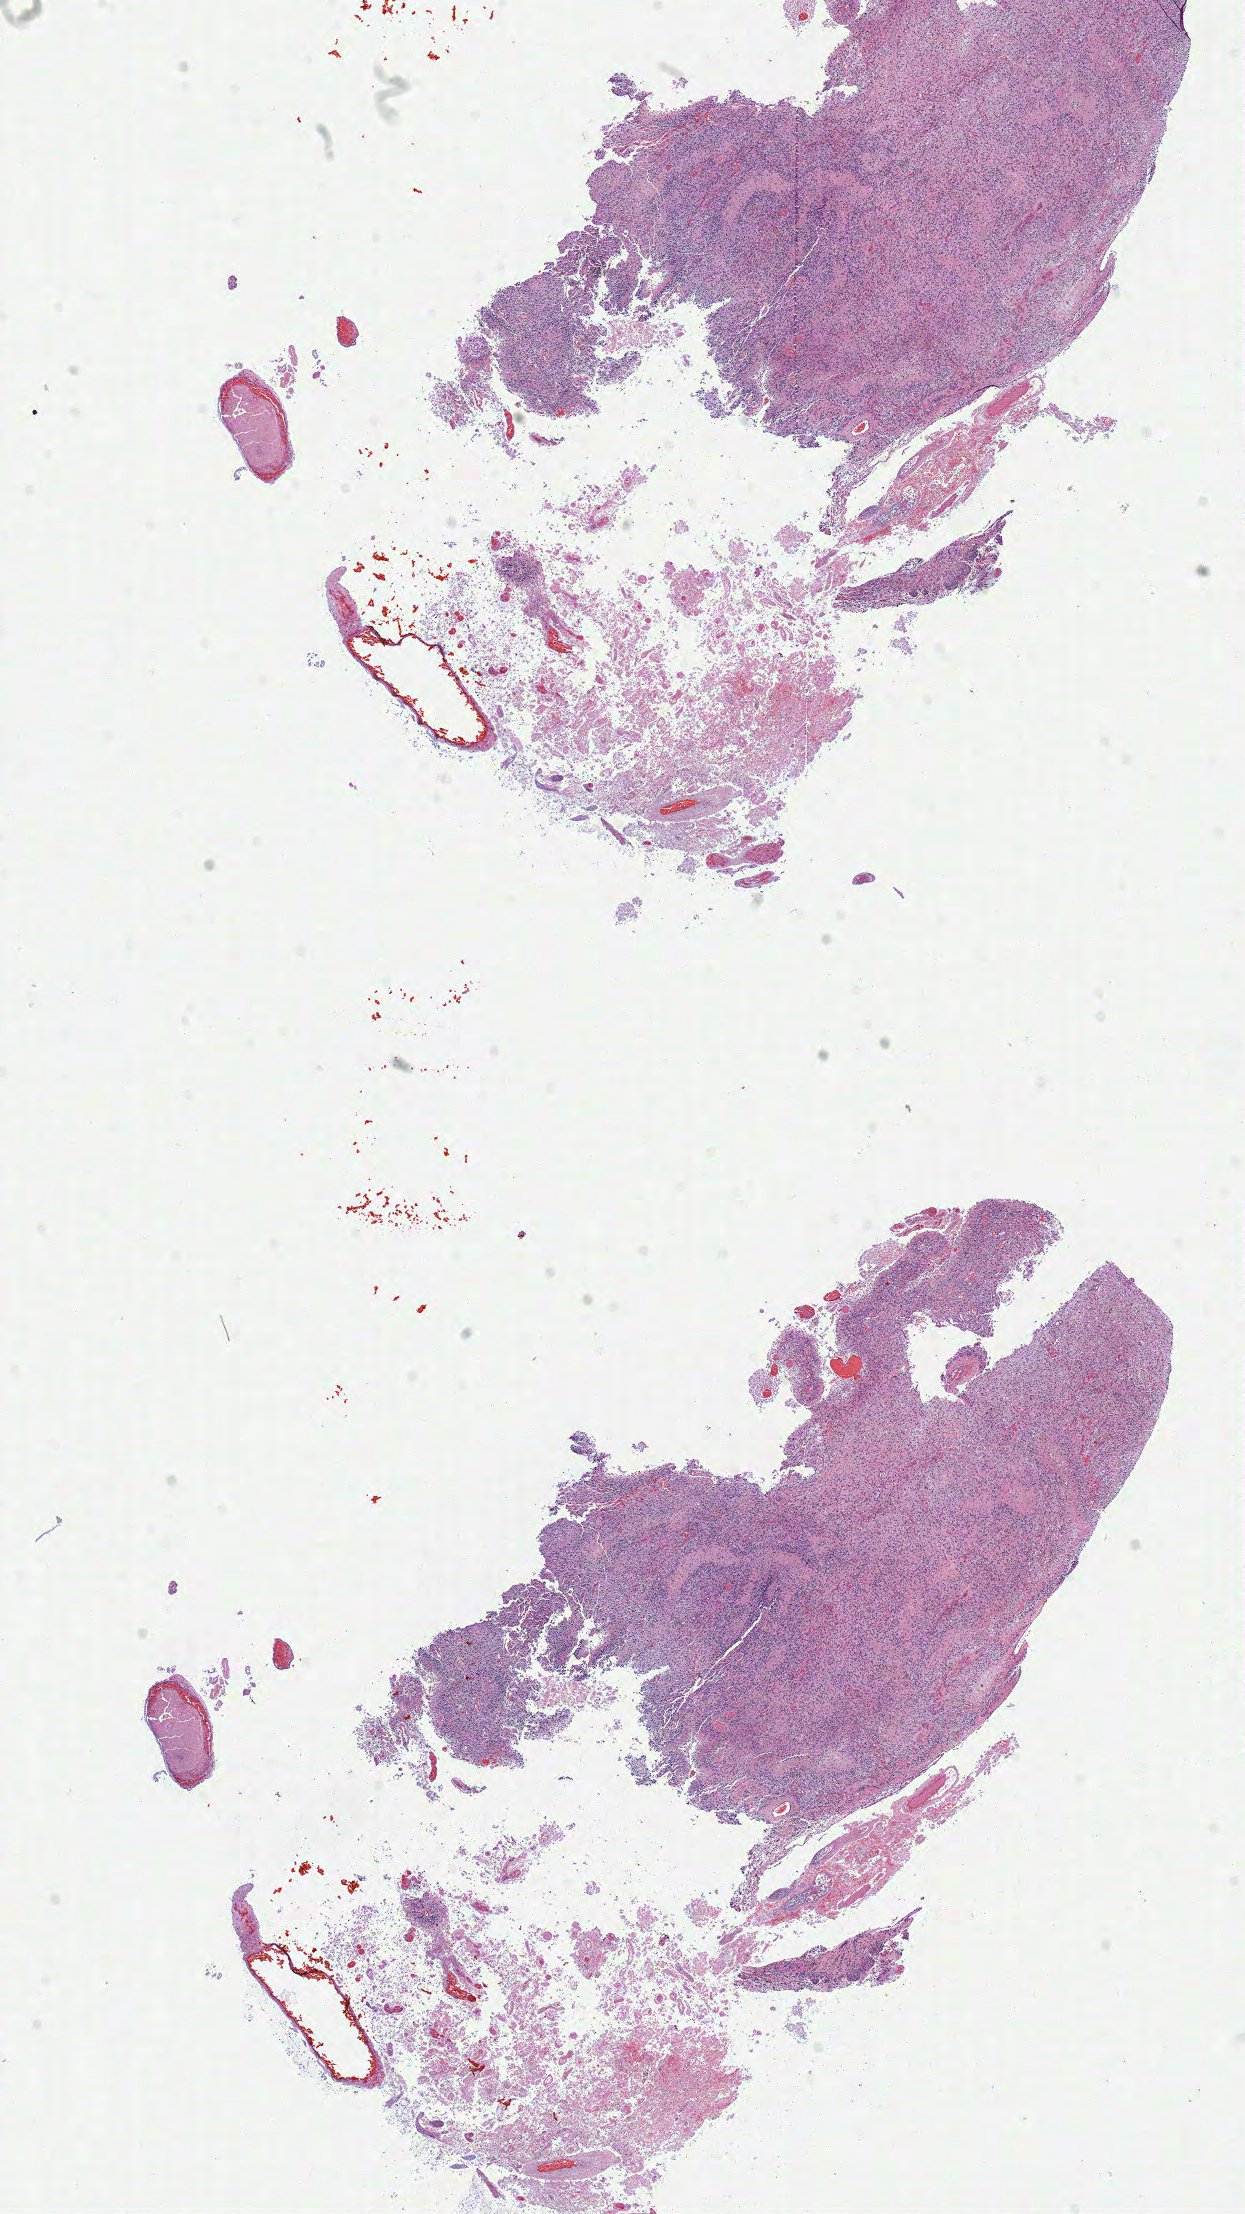
Digitized H&E-stained tissue section (whole slide), whole scanned area (about 9.8 x 17.4 mm, slide scanned at 40x) shown as a low-resolution overview. Frozen section. Primary tumour sample from the brain. Patient: female, age at initial diagnosis 64 years. Composition of this section per pathologist review: tumour cells 65%, tumour nuclei 80%, normal cells 0%, stromal cells 0%, necrosis 35%.
* pathologic diagnosis: Glioblastoma